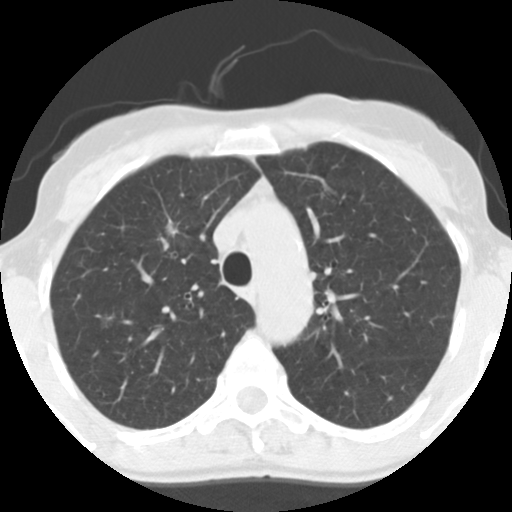
Chest CT (low-dose screening protocol), one axial image, baseline annual screen, lung window (W 1500 / L -600 HU), slice 41 of 130 in the series, 512 × 512 image matrix. Female, age 56 years at enrolment. Former smoker at enrolment.
Lesion marked by an expert reader, bounding box [x1, y1, x2, y2] px = [151, 212, 189, 252]. The exam's reader record, not a measurement of the box and not confirmed to be the same lesion: non-calcified nodule or mass ≥4 mm, right upper lobe, 12 × 9 mm, spiculated (stellate) margins, soft tissue attenuation. Official screen result: positive, change unspecified: nodule(s) >= 4 mm or enlarging nodule(s), mass(es), or other non-specific abnormalities suspicious for lung cancer. Participant outcome: lung cancer diagnosed 779 days after this screen (after the third annual screen) — adenocarcinoma, NOS, right upper lobe, moderately differentiated (G2), stage IA (AJCC 6th edition), 19 mm at pathology.